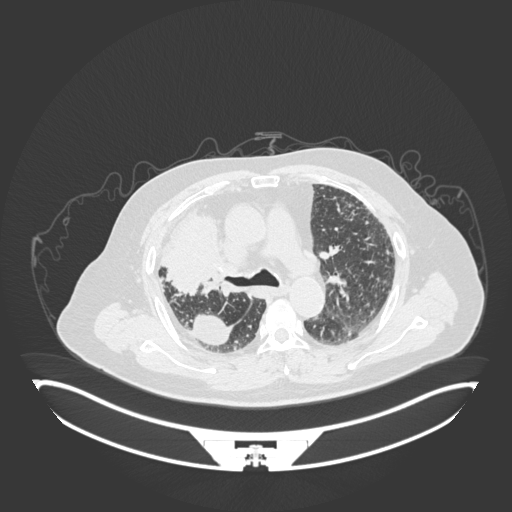
Chest CT, one axial slice. Slice 118 of 201 in the series (ordered by position). 120 kVp. Lung window (W 1500 / L -600 HU). 1 mm slice thickness. 512 × 512 image matrix, field of view 500 × 500 mm. Male patient, age 69 years. From the clinical record (not read from this slice): clinical TNM (as recorded): T4 N3 M1.
Annotated regions visible in this slice (rectangle marked by the reading radiologist):
- lung tumour (recorded histology: adenocarcinoma): bounding box [x1, y1, x2, y2] px = [161, 207, 228, 298]